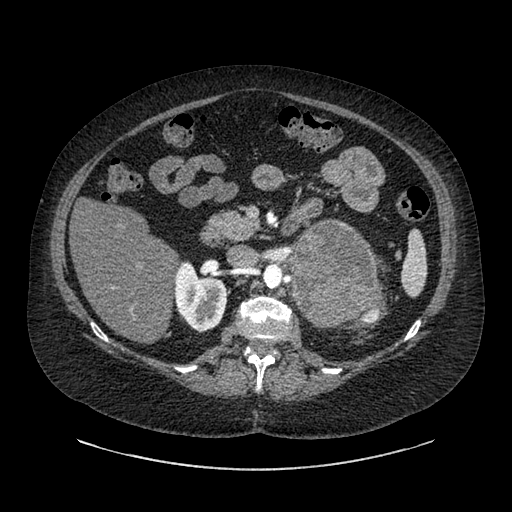
Contrast-enhanced abdominal CT, one axial slice; position 536 of 769 along the scan axis; 120 kVp; soft-tissue window (W 400 / L 40 HU); 512 × 512 image matrix. Patient: female, 61 years. From the clinical record (not read from this slice): diagnosis: adrenocortical carcinoma; tumour side: left adrenal; tumour size at pathology: 13 cm; Ki-67 index: 79 %; stage (as recorded): 2.
Annotated regions visible in this slice (semi-automatic segmentation, software-assisted and operator-edited):
- mass: bounding box <292,223,374,326> (left, top, right, bottom; pixels)